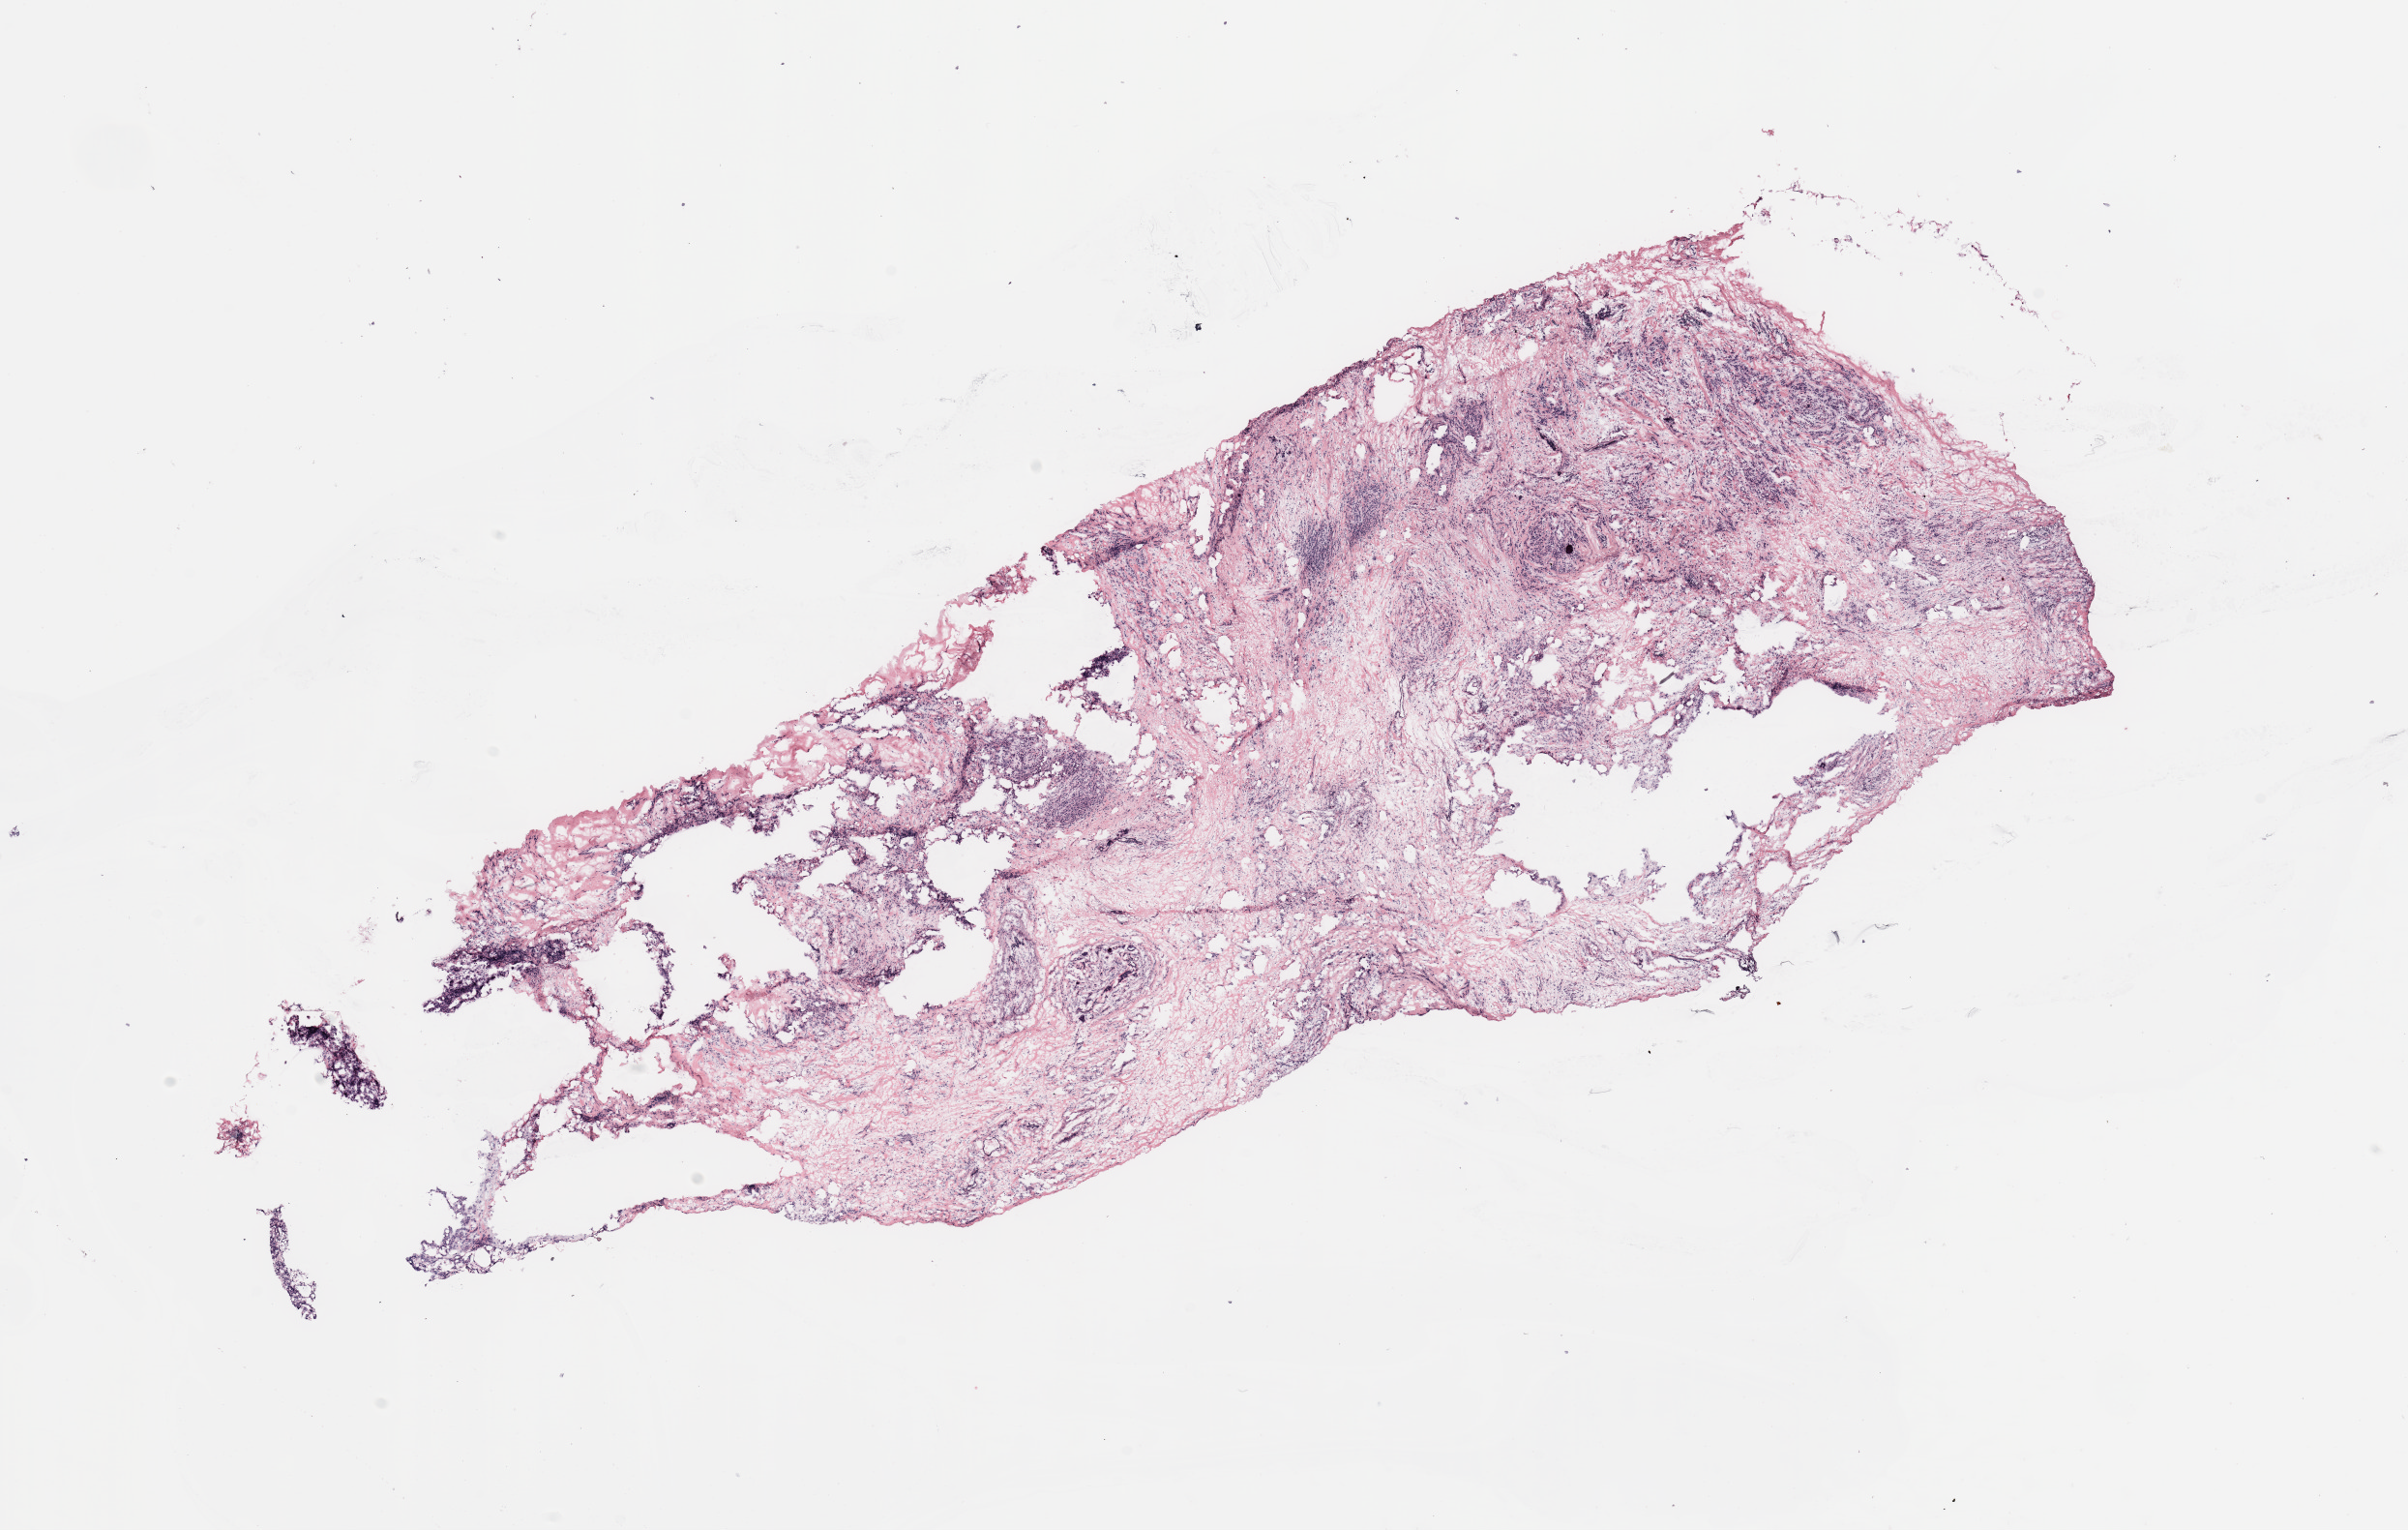
Whole-slide histology image, H&E — a low-resolution overview of the entire scanned area, about 19.7 x 12.5 mm; breast, tissue type not recorded.
Patient diagnosis (cohort enrolment): breast cancer (breast).